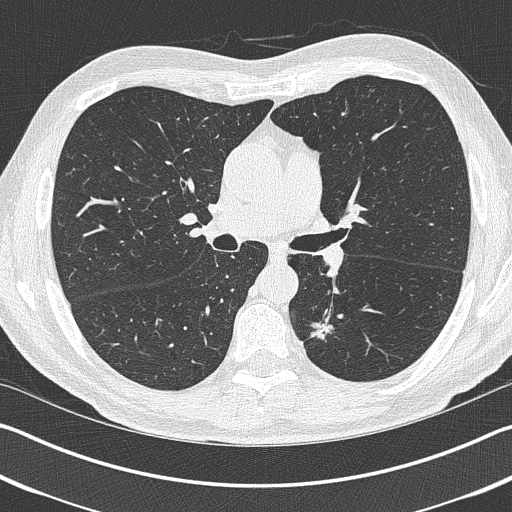
Axial slice from a low-dose chest CT screening exam, first (baseline) screen, lung window (W 1500 / L -600 HU), 1 mm slice thickness, lung (sharp) reconstruction kernel (B50f), slice 159 of 402 in the series, 512 × 512 image matrix. Male, age 69 years at enrolment. Current smoker at enrolment.
Lesion marked by an expert reader, bounding box (x1, y1, x2, y2) in pixels: (301, 309, 356, 361). Screening reader's record for this exam (one nodule recorded; not confirmed to be the boxed lesion): non-calcified nodule or mass ≥4 mm, left upper lobe, 19 × 19 mm, spiculated (stellate) margins, pre-existing on the prior screen: yes. Participant outcome: lung cancer diagnosed 202 days after this screen — non-small cell carcinoma, left lower lobe, stage IIIA (AJCC 6th edition), 20 mm at pathology.